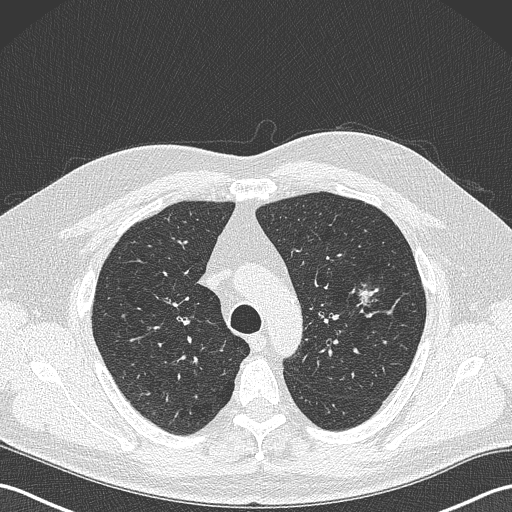
Low-dose screening chest CT, axial slice; first (baseline) screen; lung window (W 1500 / L -600 HU); 1 mm slice thickness; lung (sharp) reconstruction kernel (B50f); slice 90 of 343 in the series. Male participant, aged 61 years at enrolment. Former smoker at enrolment.
• Lesion marked by an expert reader, box from (x=350, y=282) to (x=385, y=312) px.
• The screening reader recorded 2 non-calcified nodules or masses ≥4 mm on this exam; which of them this box marks is not recorded.
• Official screen result: positive, change unspecified: nodule(s) >= 4 mm or enlarging nodule(s), mass(es), or other non-specific abnormalities suspicious for lung cancer.
• Participant outcome: lung cancer diagnosed 160 days after this screen — adenocarcinoma, NOS, left upper lobe, poorly differentiated (G3), stage IA (AJCC 6th edition), 28 mm at pathology.